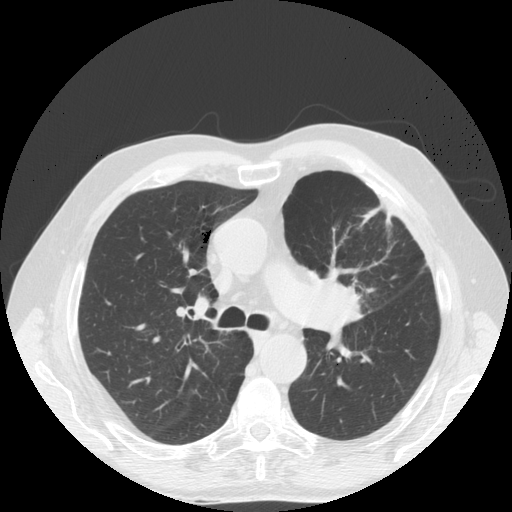
Axial slice from a low-dose chest CT screening exam; first (baseline) screen; lung window (W 1500 / L -600 HU); slice 57 of 171 in the series; 512 × 512 image matrix, field of view 380 × 380 mm. Male, age 70 years at enrolment.
Lesion marked by an expert reader, bounding box (x1, y1, x2, y2) in pixels: (291, 254, 381, 343). Reader record for this screening exam (exam-level; its link to the box is not recorded): non-calcified nodule or mass ≥4 mm, left upper lobe, 46 × 31 mm, spiculated (stellate) margins, soft tissue attenuation. Official screen result: positive, change unspecified: nodule(s) >= 4 mm or enlarging nodule(s), mass(es), or other non-specific abnormalities suspicious for lung cancer. Lung cancer was diagnosed 78 days after this screen: squamous cell carcinoma, NOS, left upper lobe, poorly differentiated (G3), stage IIIB (AJCC 6th edition), 46 mm at pathology.